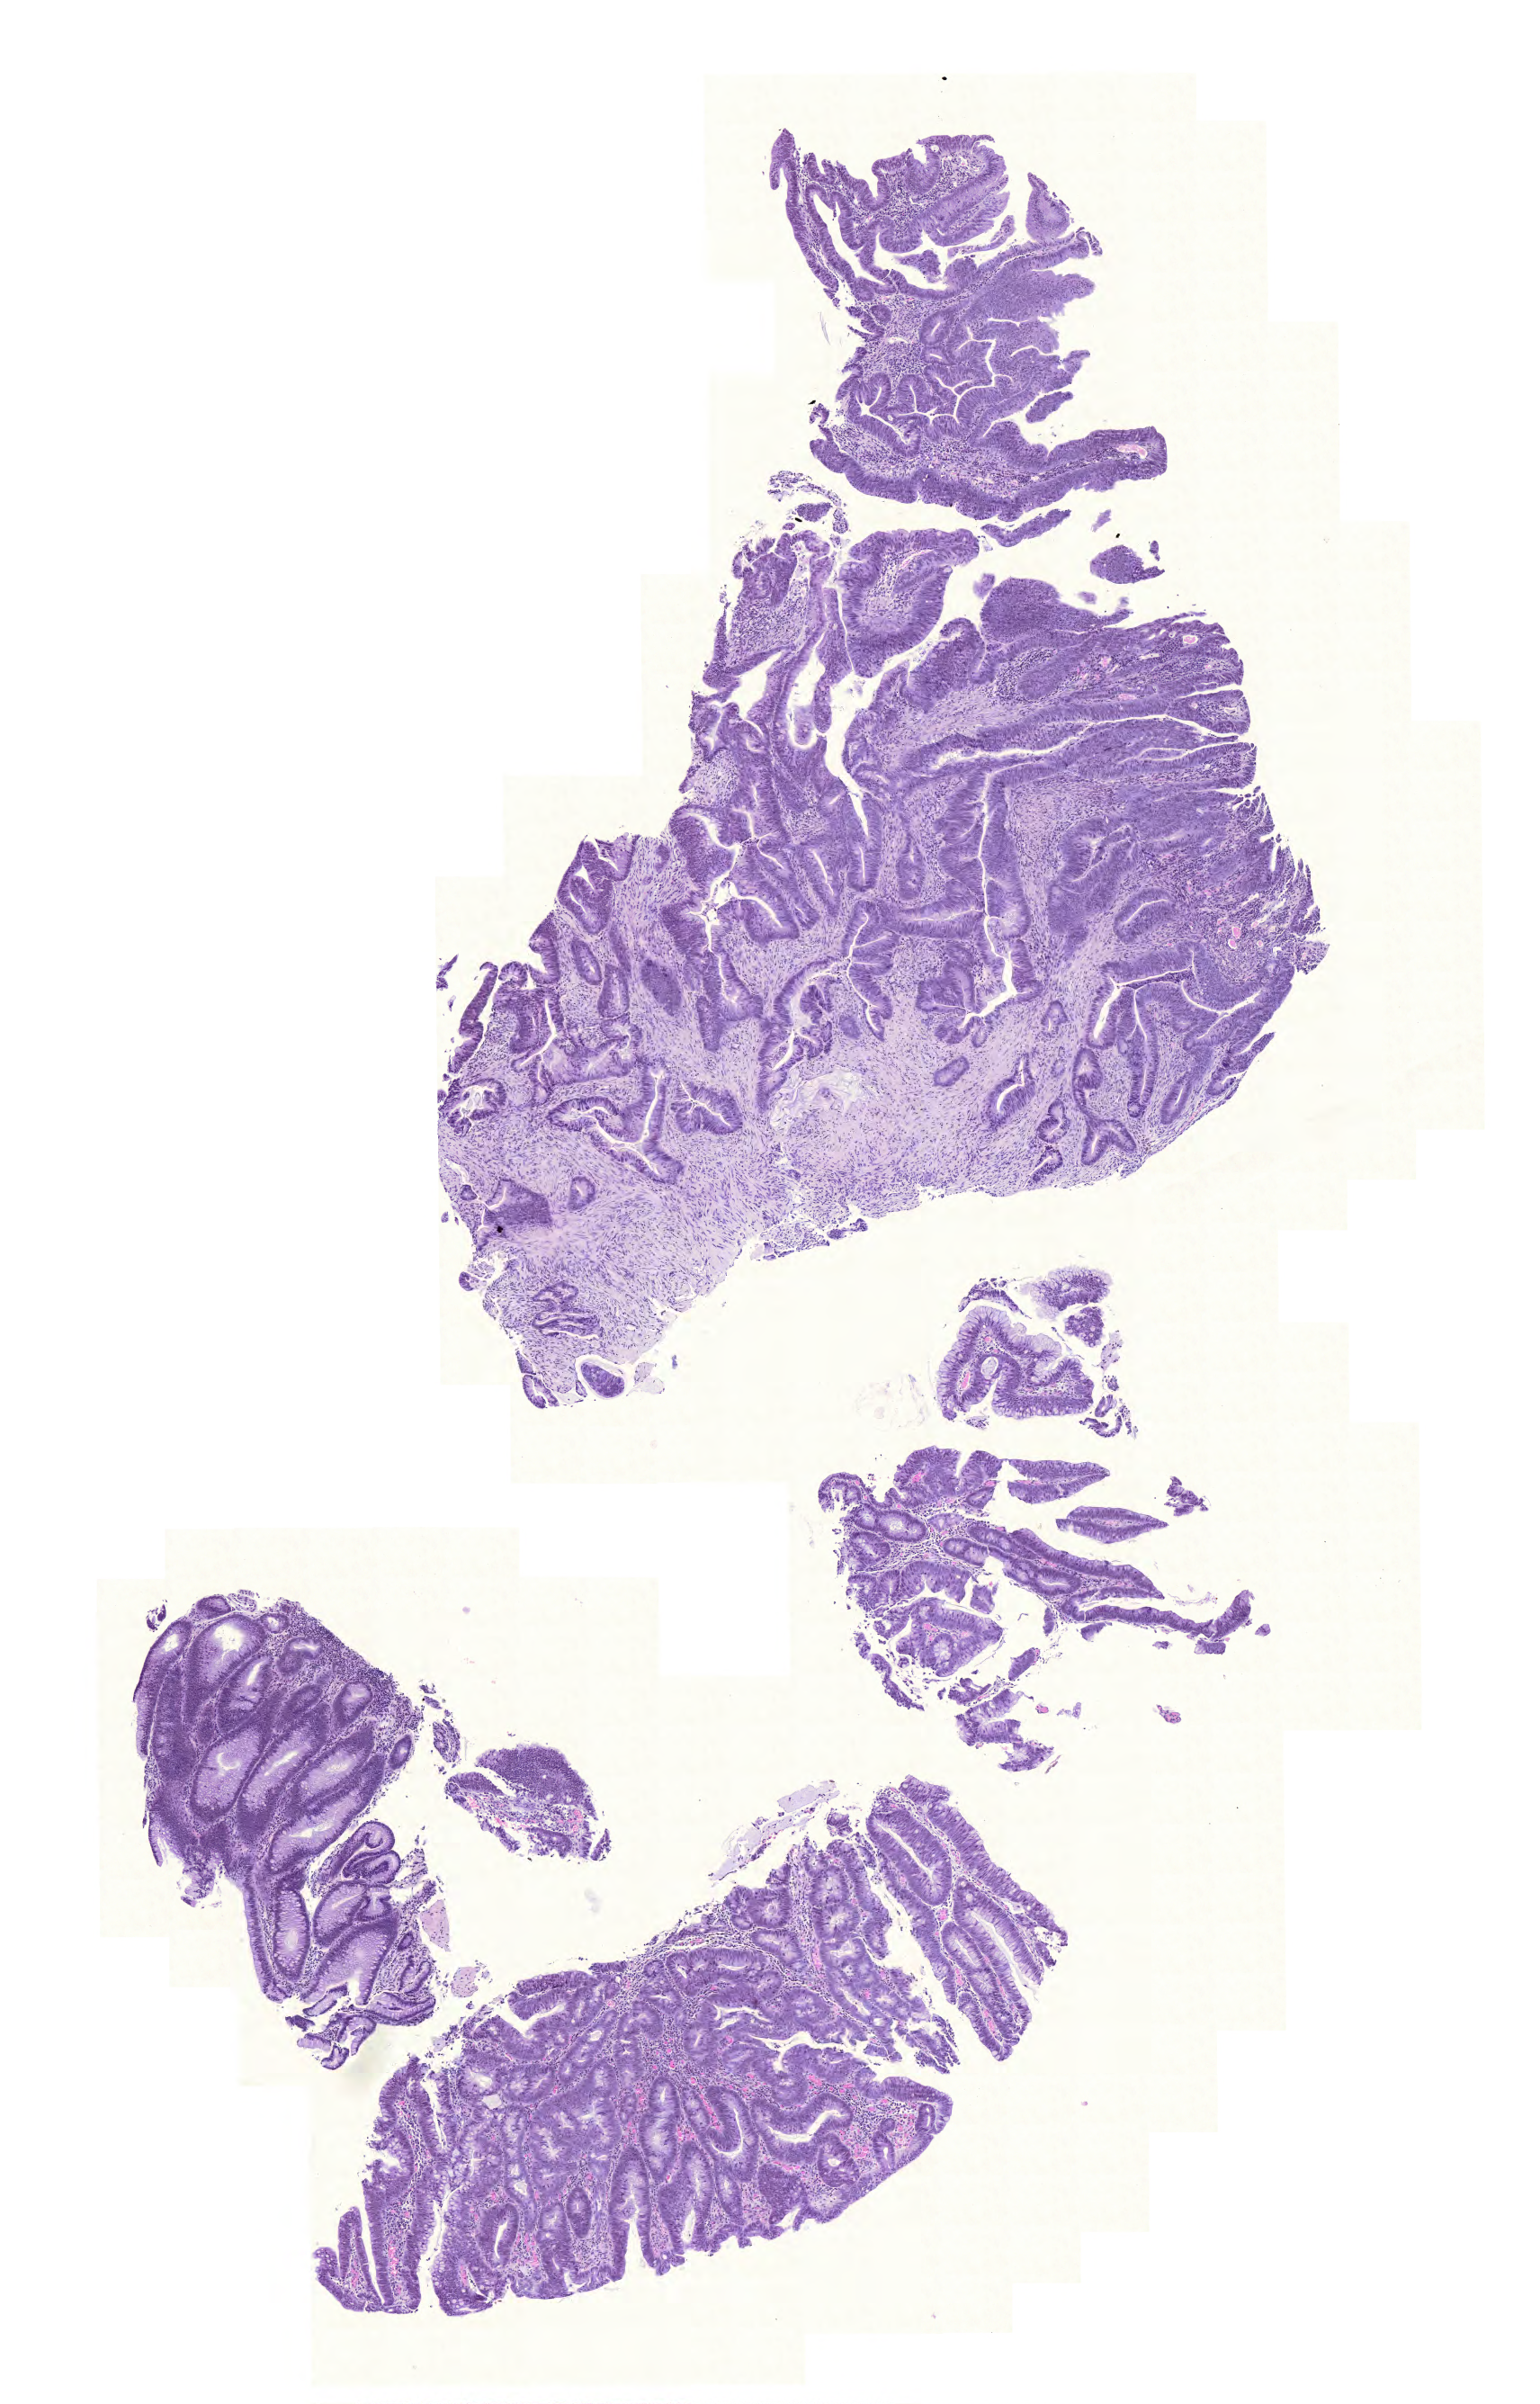
H&E-stained whole-slide image, shown as a low-resolution overview of the whole scanned area (about 6.4 x 9.9 mm, from a 20x scan). Formalin-fixed paraffin-embedded (FFPE) diagnostic section. Primary tumour sample from the rectum. Female patient; age at initial diagnosis 67 years.
AJCC pathologic stage: IIIB. Pathologic diagnosis: Mucinous adenocarcinoma.